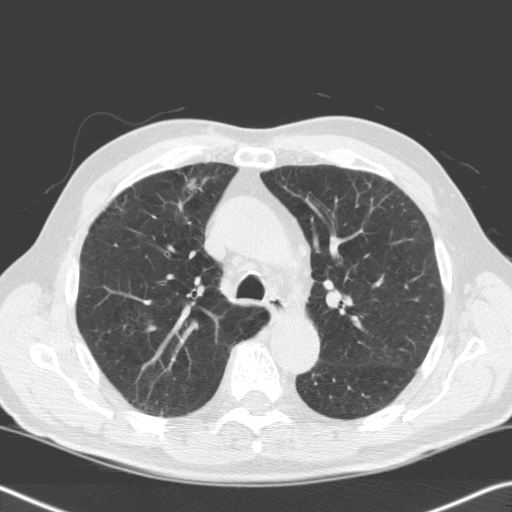
Low-dose screening chest CT, one axial slice. Lung window (W 1500 / L -600 HU). 3.2 mm slice thickness. 512 × 512 image matrix, field of view 343 × 343 mm.
Structures marked on this image (outlined manually by an expert reader):
- lesion 1 (tumor, upper lobe of right lung): bounding box [x1, y1, x2, y2] px = [188, 180, 196, 190]